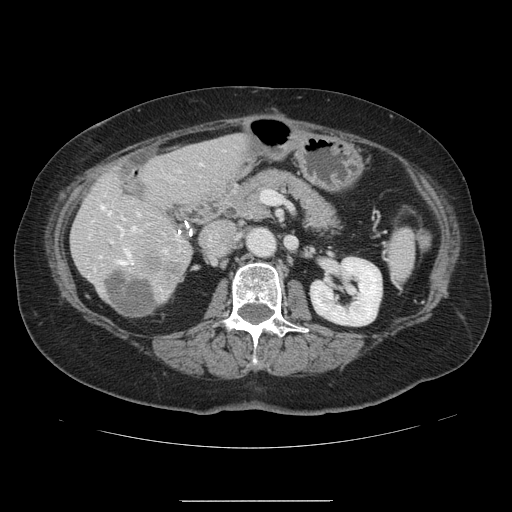
Contrast-enhanced abdominal CT, one axial slice; position 55 of 141 along the scan axis; 120 kVp; intravenous contrast given; soft-tissue window (W 400 / L 40 HU); 2.5 mm slice thickness; 512 × 512 image matrix, field of view 393 × 393 mm. Female patient, age 74 years. Case-level facts recorded for this patient, not image findings: diagnosis: colorectal cancer liver metastases, imaged before liver resection; multiple liver metastases: yes; largest metastasis: 7 cm; chemotherapy before resection: no.
Structures marked on this image (manually delineated by an expert):
- hepatic veins: bounding box <101,205,136,264> (left, top, right, bottom; pixels)
- liver: <72,136,249,318>
- planned liver remnant (the part of the liver to remain after resection): <103,136,249,318>
- portal vein (with intrahepatic branches): <110,163,202,252>
- liver metastasis: <109,272,159,315>
- liver metastasis: <143,255,186,283>